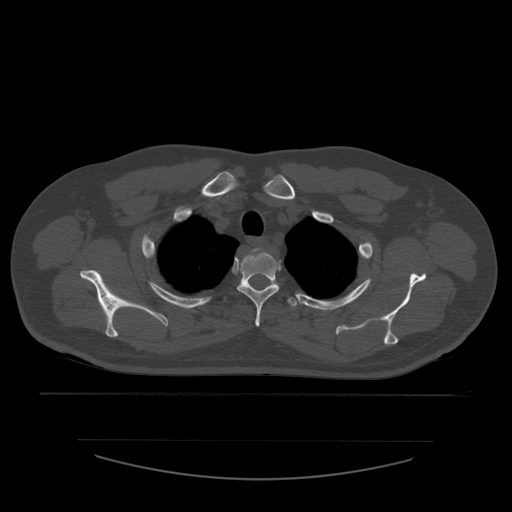
CT including the spine, one axial slice; position 450 of 532 along the scan axis; bone window (W 1800 / L 400 HU); 1.25 mm slice thickness; 512 × 512 image matrix, field of view 441 × 441 mm. Patient age 44 years. From the clinical record (not read from this slice): primary cancer: soft tissue sarcoma.
Structures marked on this image (semi-automatic segmentation, software-assisted and operator-edited):
- T2 vertebra: box from (x=237, y=250) to (x=280, y=327) px
- T3 vertebra: (x=288, y=297)–(x=297, y=307)